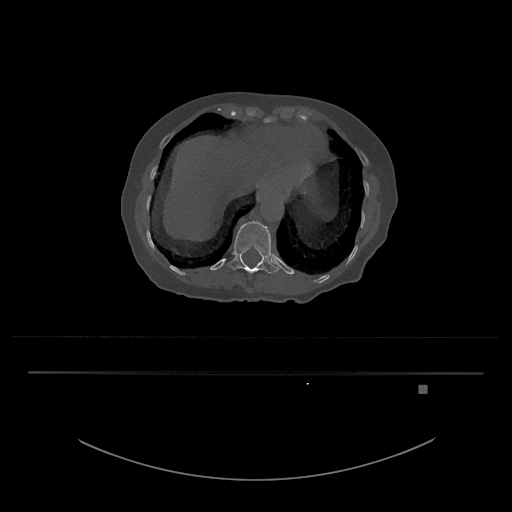
CT including the spine, one axial slice. Position 617 of 797 along the scan axis. Bone window (W 1800 / L 400 HU). 512 × 512 image matrix. Female patient, age 57 years. Case-level facts recorded for this patient, not image findings: primary cancer: cervical.
Structures marked on this image (semi-automatically segmented with operator editing):
- T12 vertebra: bounding box [x1, y1, x2, y2] px = [227, 221, 279, 274]